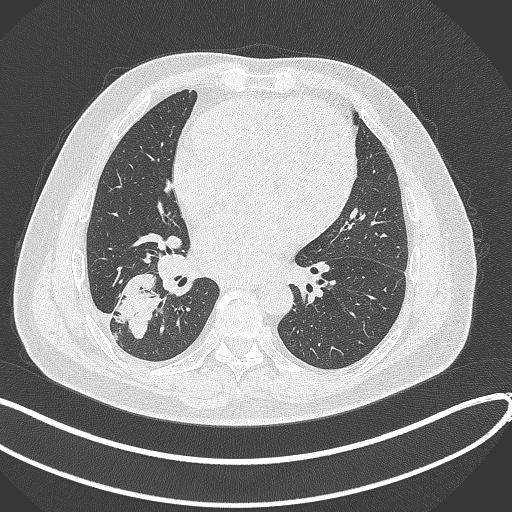
Chest CT, one axial slice; slice 160 of 360 in the series (ordered by position); reconstruction kernel B70f; lung window (W 1500 / L -600 HU); 1 mm slice thickness; 512 × 512 image matrix, field of view 400 × 400 mm. Male patient, age 59 years.
Structures marked on this image (rectangle marked by the reading radiologist):
- lung tumour (recorded histology: adenocarcinoma): box from (x=113, y=268) to (x=164, y=343) px